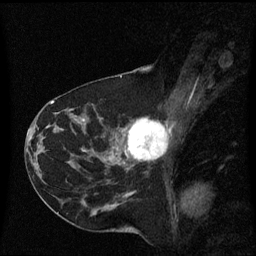
Breast MRI (dynamic contrast-enhanced), one sagittal slice; slice 31 of 60 in the series (ordered by position); dynamic contrast-enhanced series, image 2 of 3 at this slice position (ordered by acquisition); 1.5 T; TE 4.2 ms, TR 8.4 ms; 2 mm slice thickness; 256 × 256 image matrix. Patient: female, 41 years. Case-level facts recorded for this patient, not image findings: setting: breast cancer imaged before/during neoadjuvant chemotherapy; receptor status: triple-negative.
Annotated regions visible in this slice (semi-automatic segmentation, software-assisted and operator-edited):
- analysis volume of interest (the breast-tissue region the enhancement analysis was run in; not a lesion): bounding box [x1, y1, x2, y2] px = [116, 118, 169, 171]
- tumour enhancement mask (voxels above the 70 % enhancement threshold inside the analysis volume of interest): [127, 118, 167, 161]